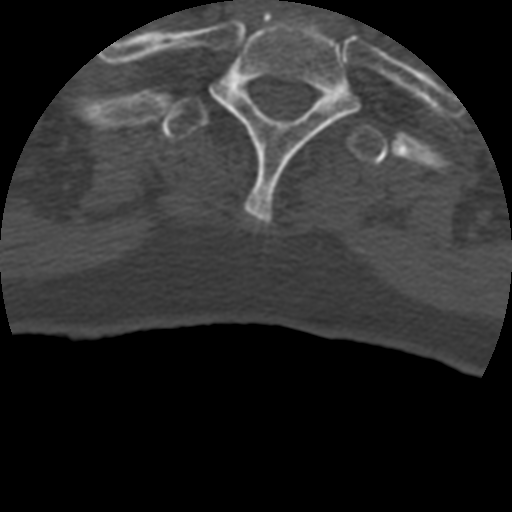
CT including the spine, one axial slice. Position 381 of 399 along the scan axis. Bone window (W 1800 / L 400 HU). 512 × 512 image matrix, field of view 160 × 160 mm. Patient age 69 years. Case-level facts recorded for this patient, not image findings: primary cancer: prostate.
Outlined on this slice (semi-automatically segmented with operator editing):
- T1 vertebra: bounding box [x1, y1, x2, y2] px = [210, 17, 360, 225]
- T2 vertebra: [161, 96, 388, 165]